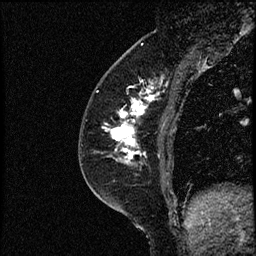
Breast MRI (dynamic contrast-enhanced), one sagittal slice; position 26 of 52 along the scan axis; dynamic contrast-enhanced study with each time point stored as its own series, time point 2 of 3 at this slice position (early post-contrast, ordered by acquisition time); 1.5 T; TE 4.2 ms, TR 17.6 ms; 256 × 256 image matrix, field of view 200 × 200 mm. Female patient, age 49 years. From the clinical record (not read from this slice): setting: breast cancer imaged before/during neoadjuvant chemotherapy; receptor status: HER2-positive.
Structures marked on this image (semi-automatic segmentation, software-assisted and operator-edited):
- analysis volume of interest (the breast-tissue region the enhancement analysis was run in; not a lesion): bounding box (x1, y1, x2, y2) in pixels: (85, 65, 182, 175)
- tumour enhancement mask (voxels above the 100 % enhancement threshold inside the analysis volume of interest): (106, 95, 158, 160)